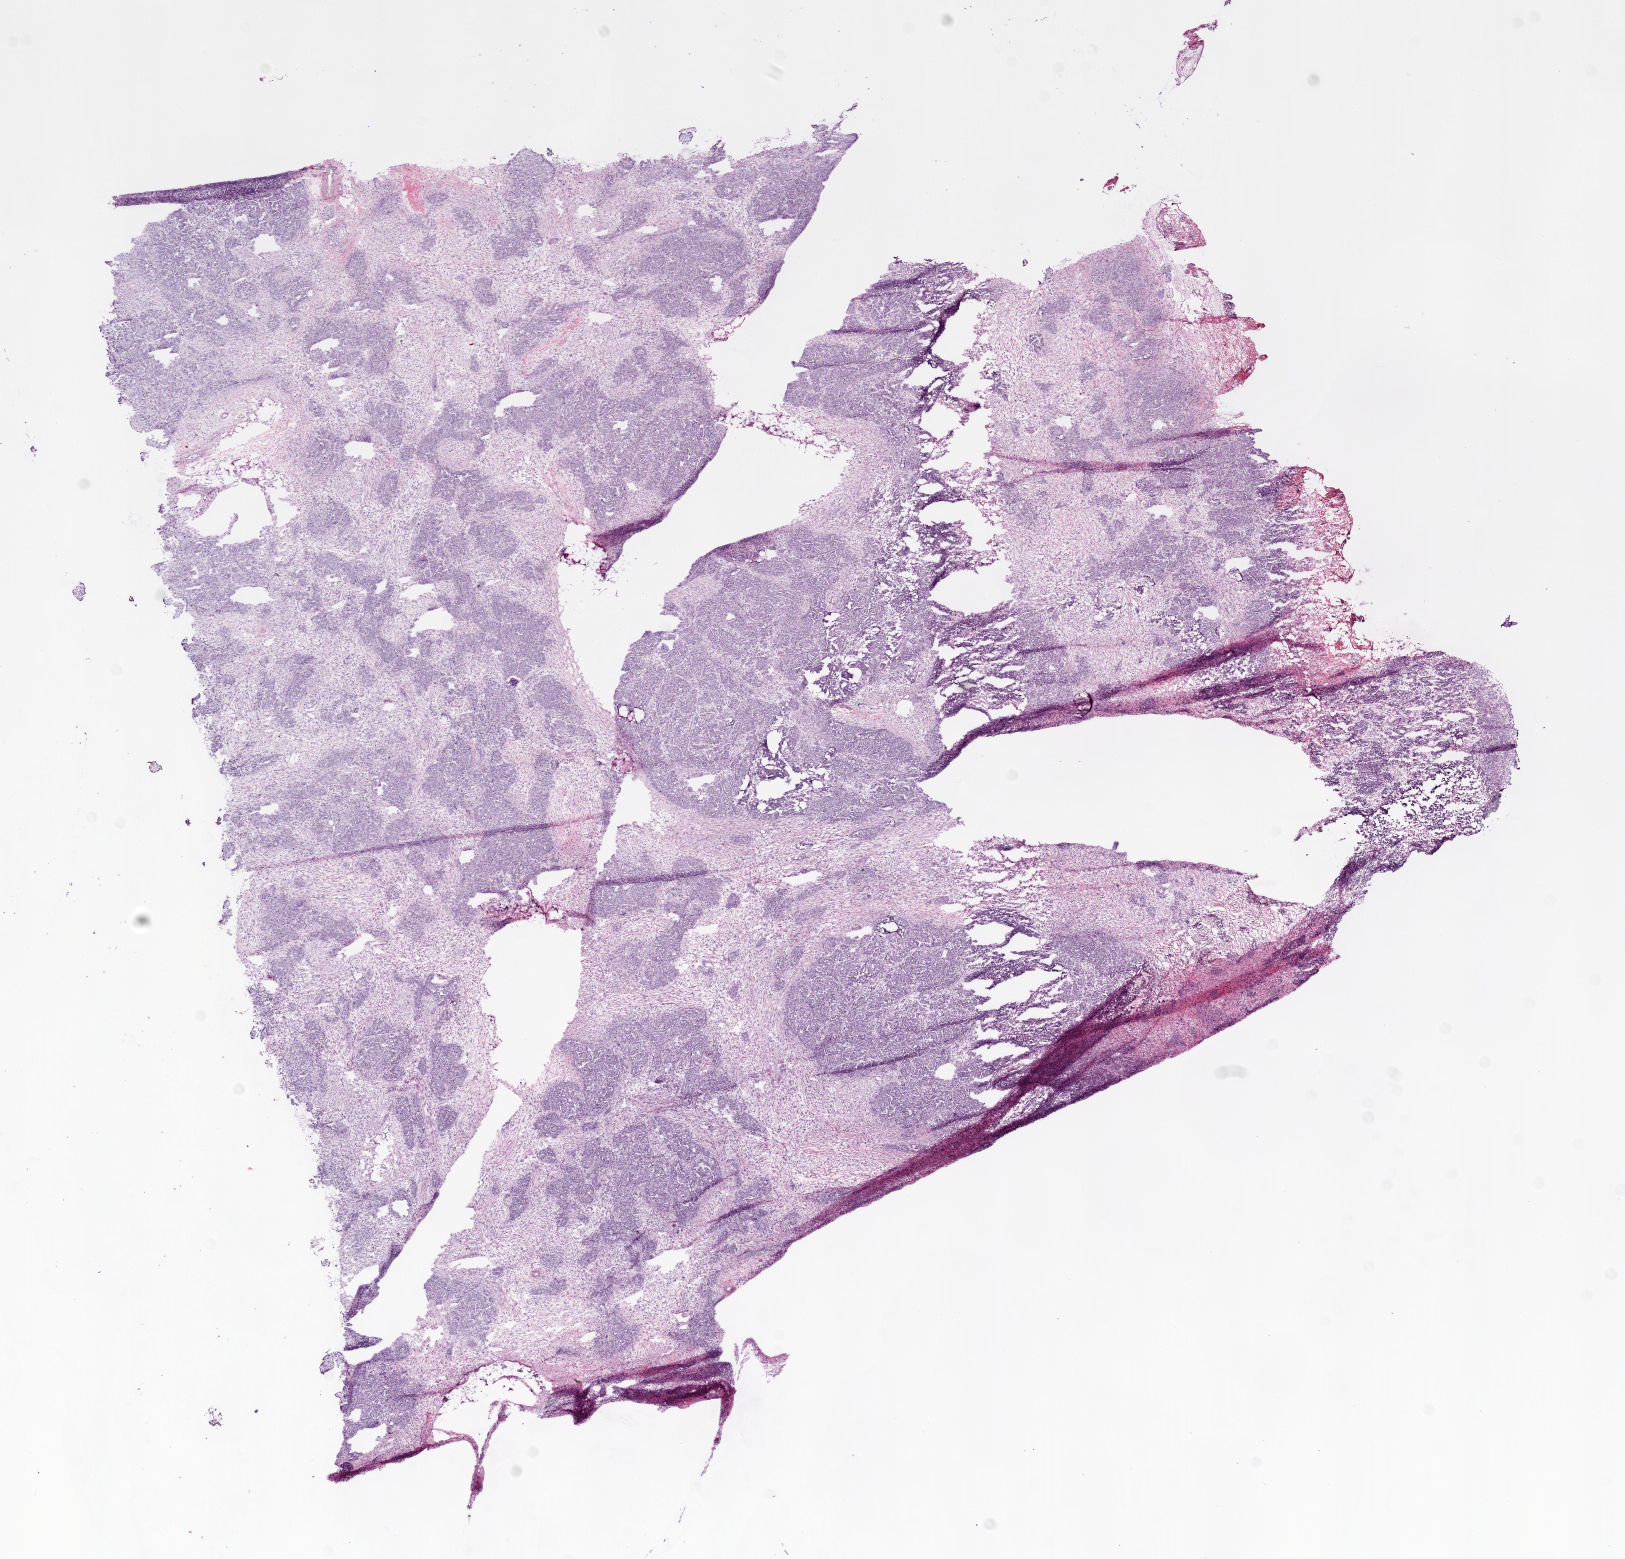
Digitized H&E-stained tissue section (whole slide) — shown as a low-resolution overview of the whole scanned area (about 13.0 x 12.5 mm); frozen section from the bottom of the tissue portion; ovary, primary tumour sample. Female patient; age at initial diagnosis 67 years. Histologic grade: G2 (moderately differentiated). Composition of this section per pathologist review: tumour cells 80%, tumour nuclei 80%, normal cells 0%, stromal cells 15%, necrosis 5%.
• FIGO stage: IIIC
• laterality: bilateral
• pathologic diagnosis: Serous cystadenocarcinoma, NOS